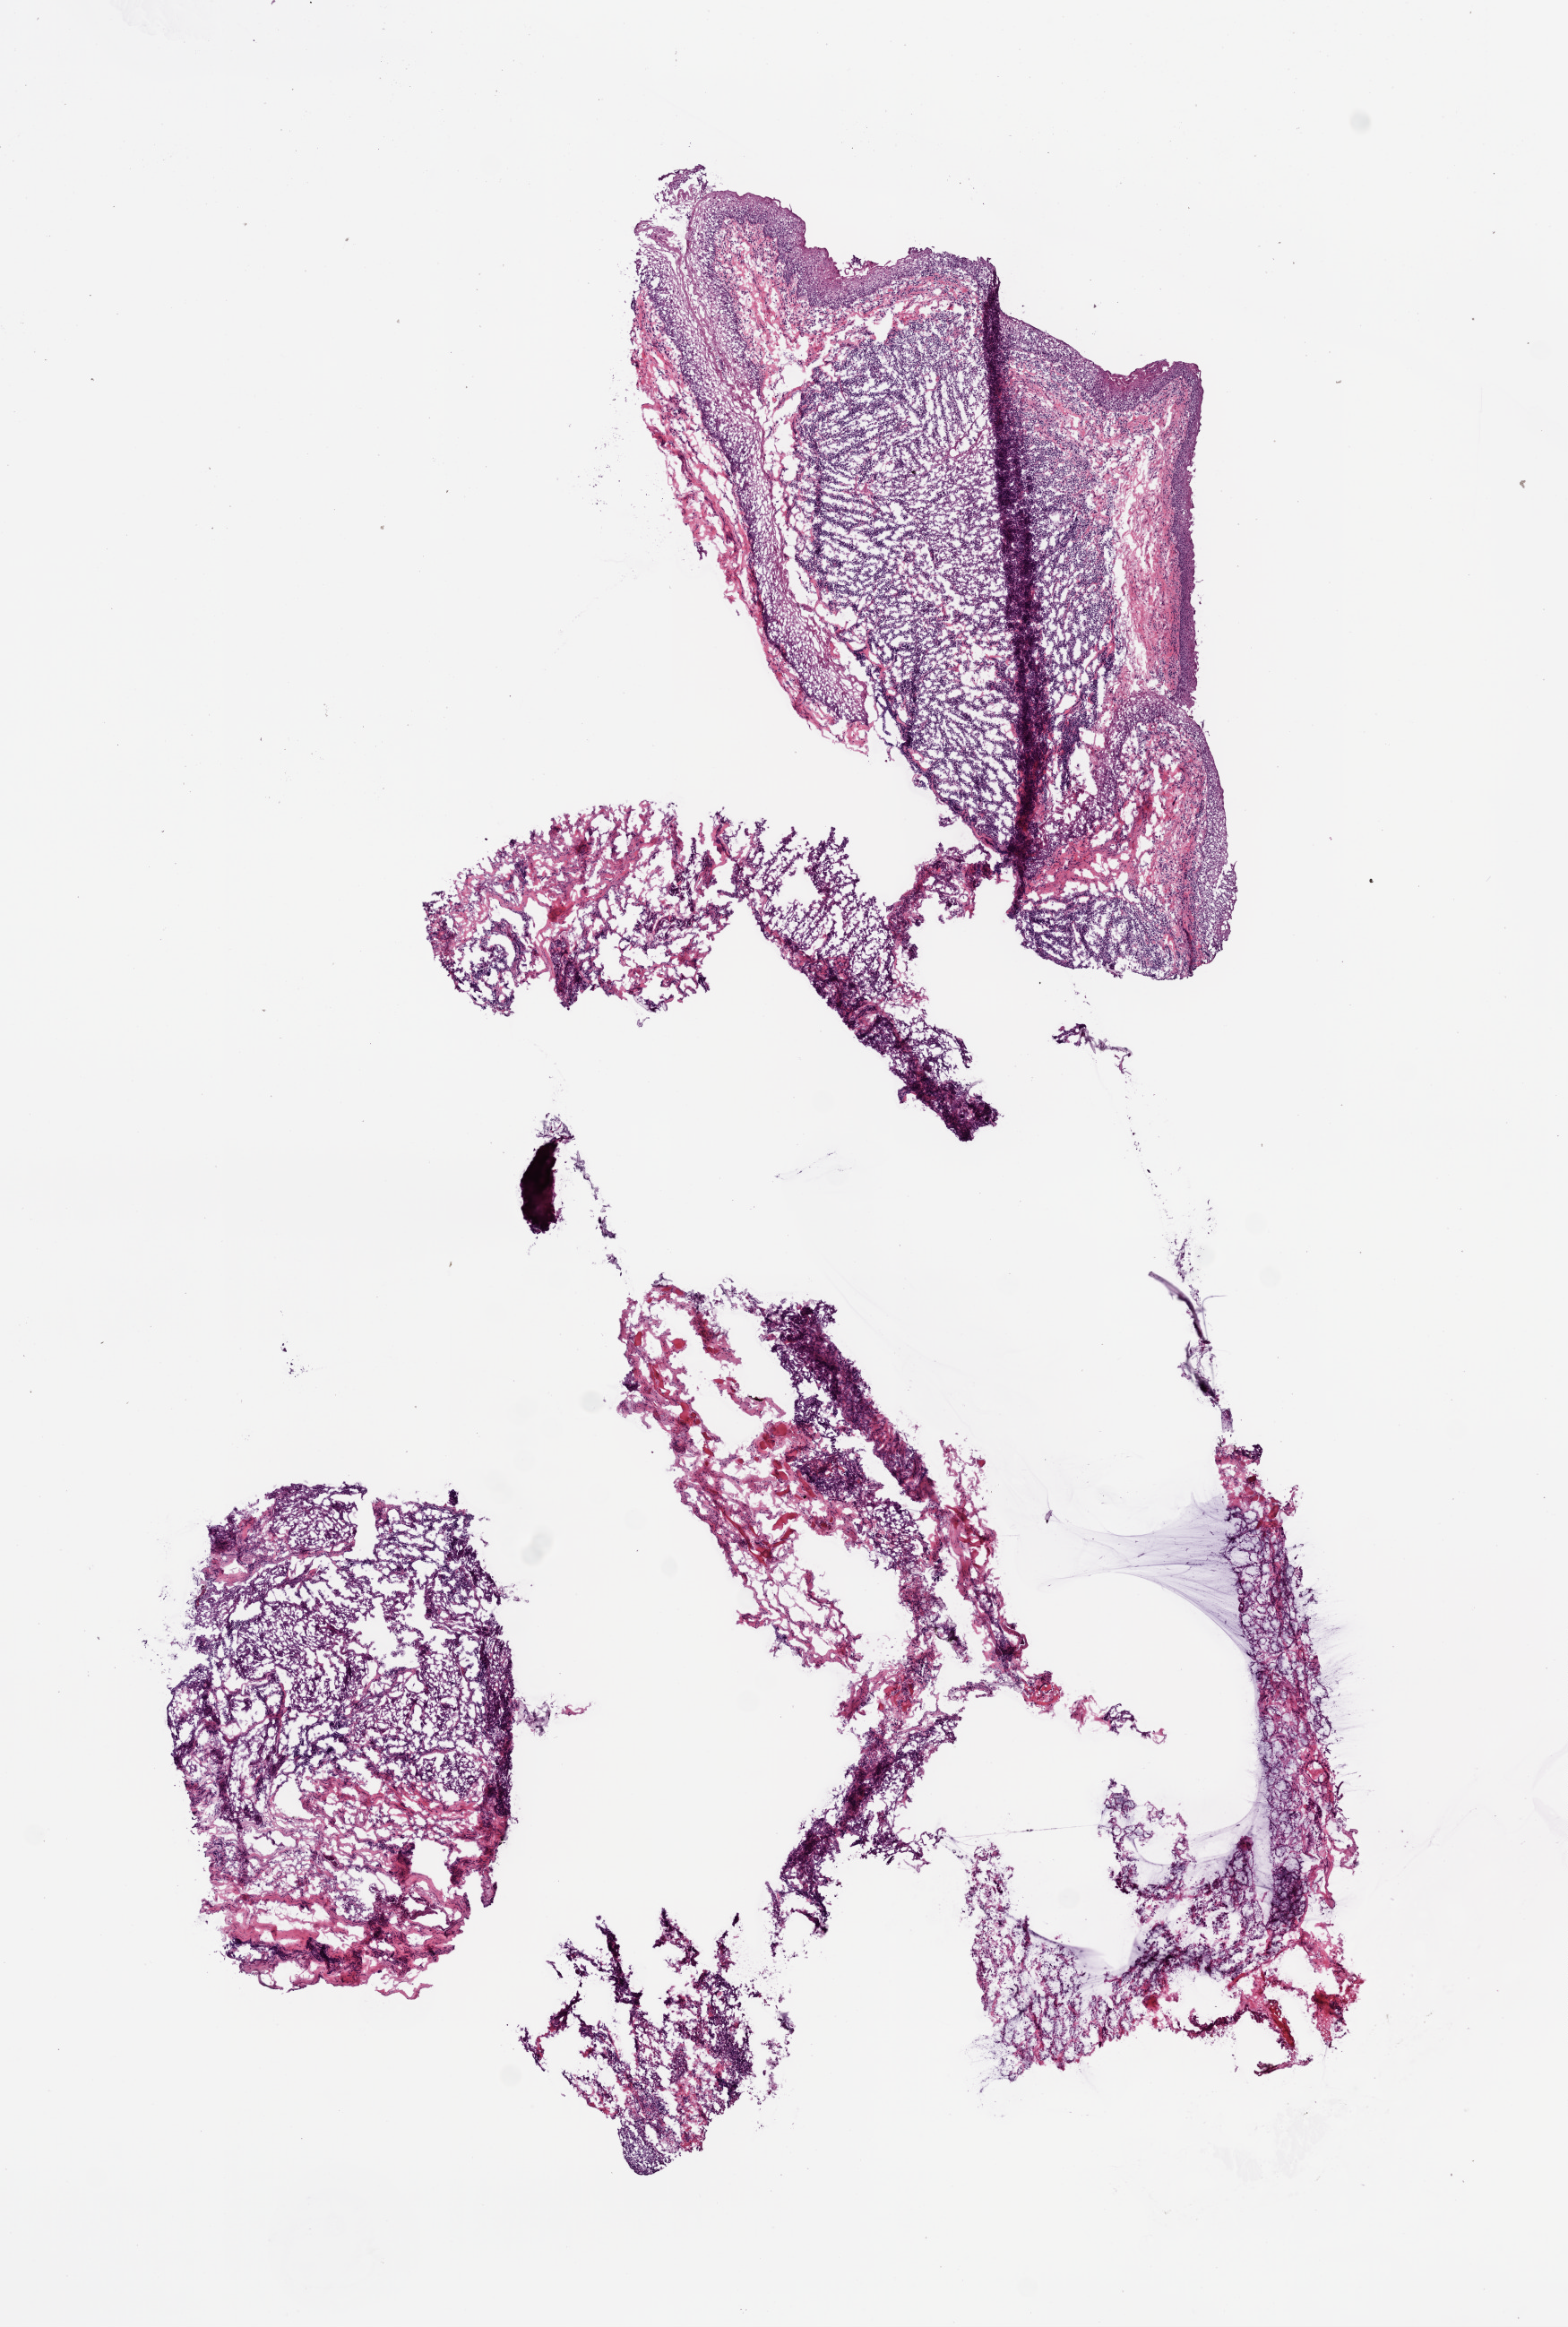
Digitized H&E tissue section (whole slide), a low-resolution overview of the entire scanned area, about 7.0 x 10.4 mm (slide scanned at 20x), frozen section from the bottom of the tissue portion, head and neck, primary tumour sample. Patient: female, age at initial diagnosis 56 years. Histologic grade: G3 (poorly differentiated). Slide review estimates, as recorded: tumour cells 80%, tumour nuclei 75%, normal cells 10%, stromal cells 10%, necrosis 0%.
* AJCC pathologic stage: IVA (6th edition)
* diagnosis: Squamous cell carcinoma, NOS (tonsil, NOS)